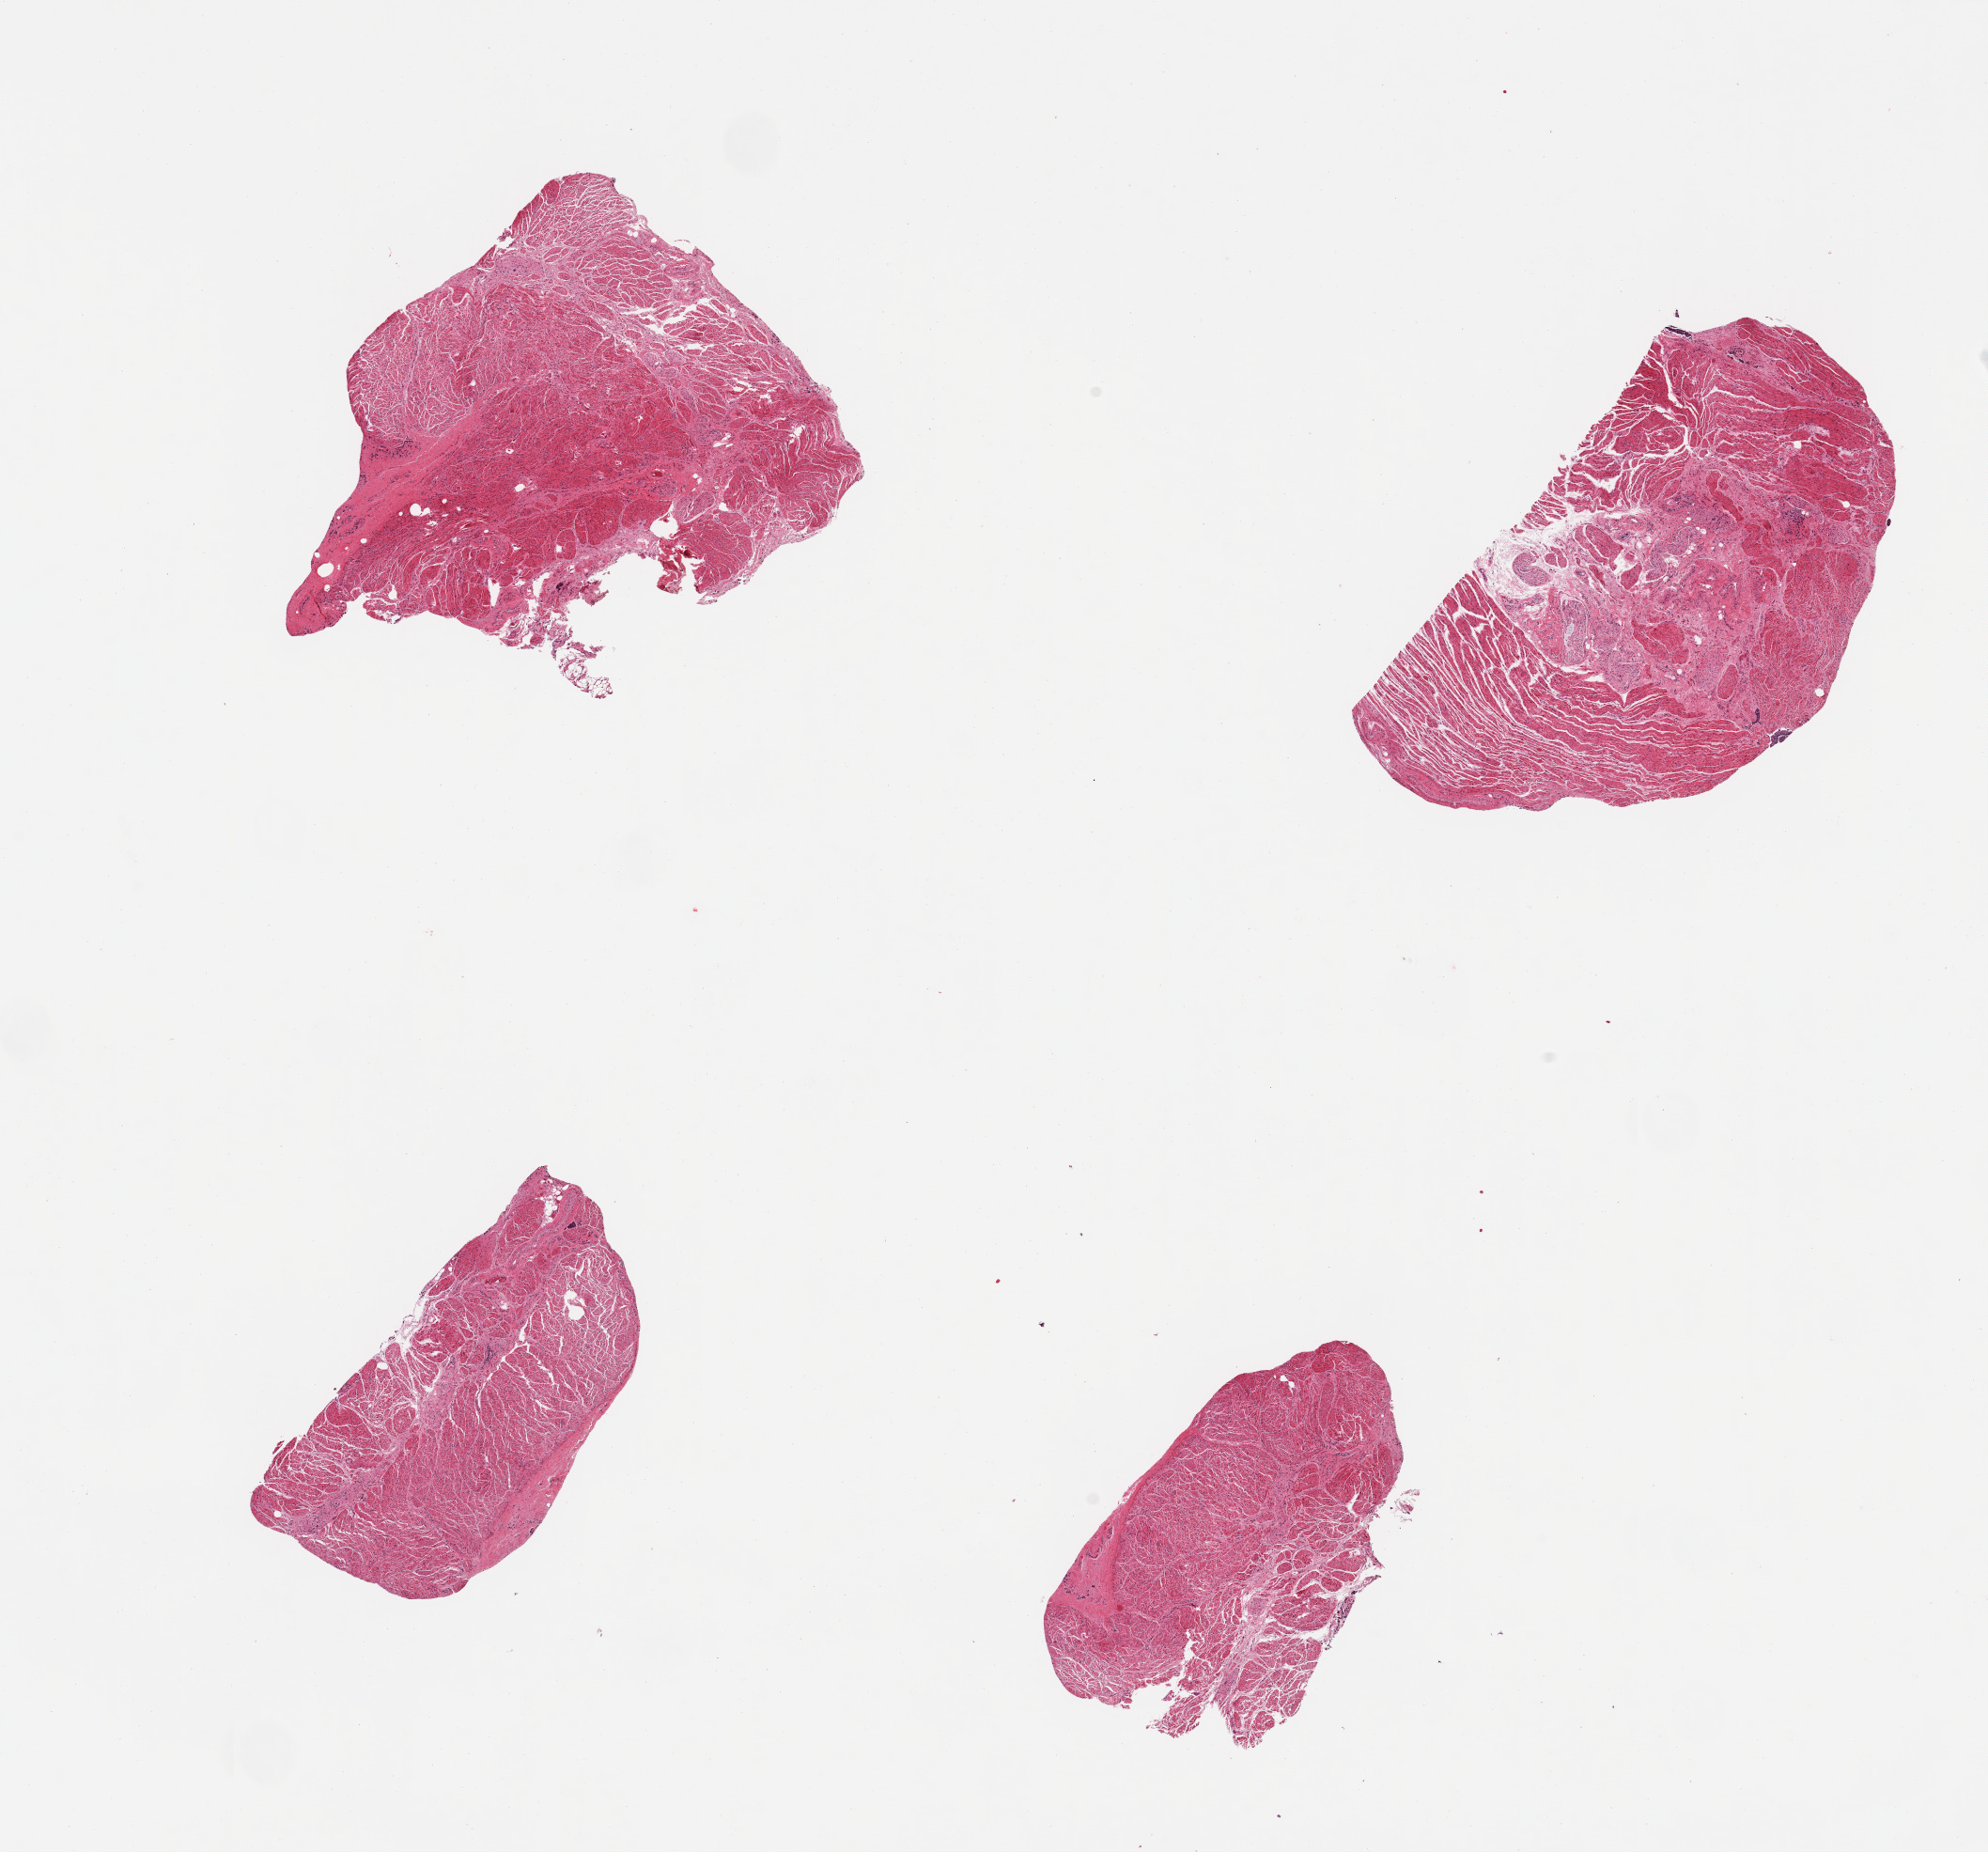
Digitized H&E-stained section — a low-resolution overview of the entire scanned area, about 16.7 x 15.6 mm; PAXgene-fixed paraffin-embedded (PFPE) section; sampled site (target tissue): esophageal muscle; donor tissue sample. Donor: female.
- reviewer comment on this tissue sample: 4 pieces; well trimmed, detached fragment of squamous epithelium